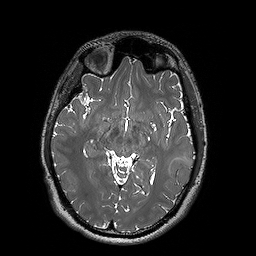
Brain MRI from a brain-tumour surgery series, one axial slice. Position 96 of 192 along the scan axis. 256 × 256 image matrix, field of view 250 × 250 mm. From the clinical record (not read from this slice): histopathology: Oligodendroglioma; WHO grade: 2; IDH mutation: yes; tumour location: Left Posterior Temporal.
Outlined on this slice (expert manual segmentation):
- tumour: bounding box (x1, y1, x2, y2) in pixels: (159, 155, 193, 173)